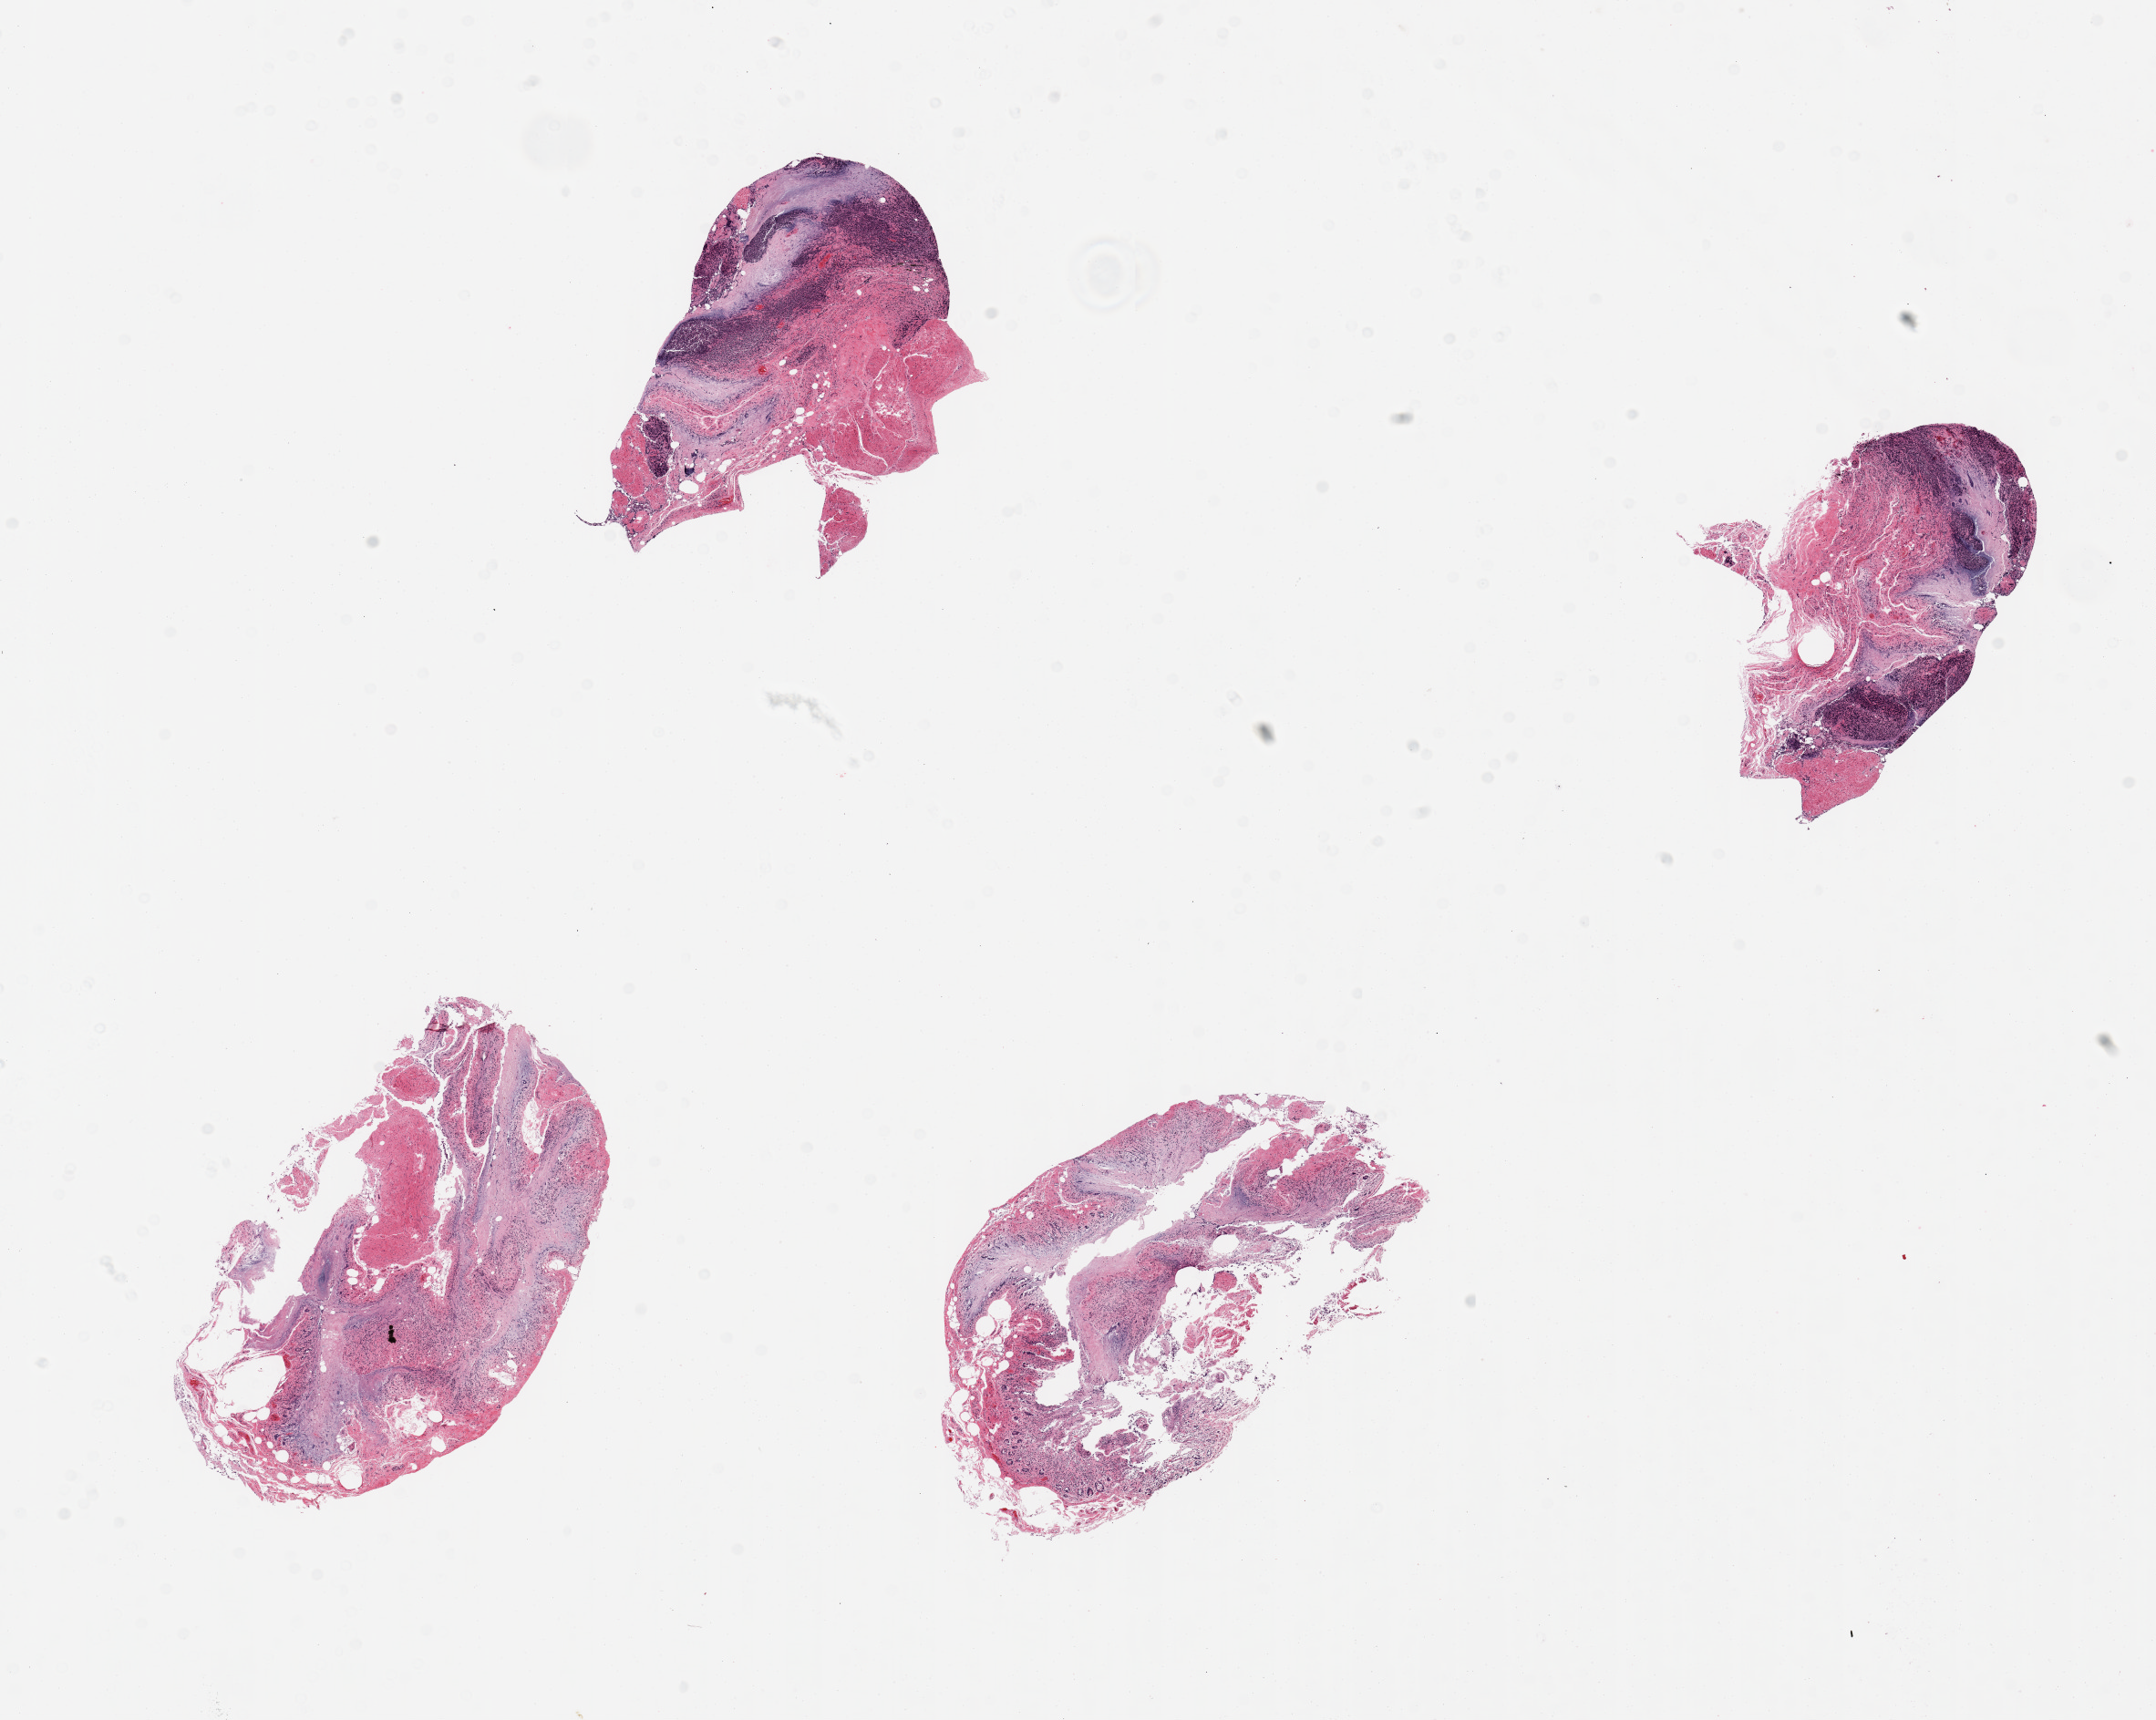
Whole-slide image, hematoxylin and eosin (H&E) stain, brightfield — shown as a low-resolution overview of the whole scanned area (about 18.7 x 14.9 mm); PAXgene-fixed paraffin-embedded (PFPE) section; section of ileum (target tissue); tissue donor sample. Donor: male.
* review note (as recorded): 4 pieces; mucosal epithelium totally autolyzed; lymphoid aggregares persist, up to ~30% of 2 sections